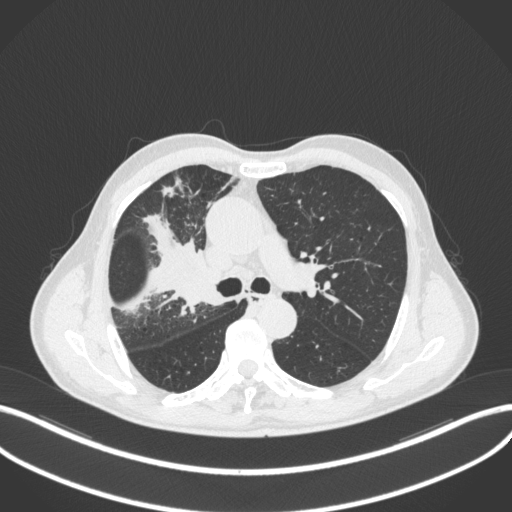
Chest CT, one axial slice. Slice 316 of 490 in the series (ordered by position). 120 kVp. Lung window (W 1500 / L -600 HU). 1 mm slice thickness. 512 × 512 image matrix, field of view 400 × 400 mm. Male patient, age 69 years. Case-level facts recorded for this patient, not image findings: clinical TNM (as recorded): T2a N0 M0.
Outlined on this slice (bounding box drawn by a radiologist):
- lung tumour (recorded histology: adenocarcinoma): bounding box (x1, y1, x2, y2) in pixels: (172, 264, 219, 311)